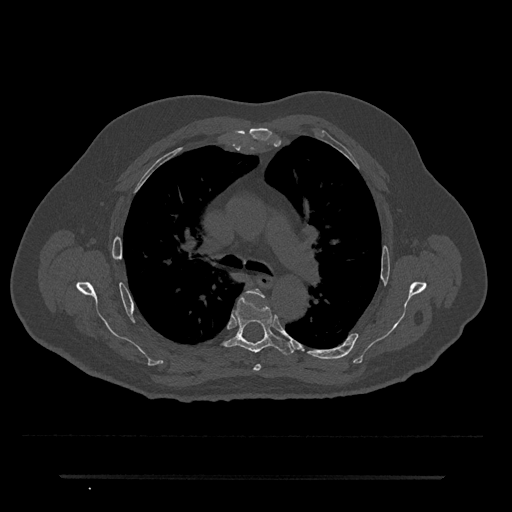
CT including the spine, one axial slice. Position 489 of 797 along the scan axis. Reconstruction kernel Br40s/3. Bone window (W 1800 / L 400 HU). 512 × 512 image matrix. Male patient, age 69 years. Case-level facts recorded for this patient, not image findings: primary cancer: prostate.
Structures marked on this image (semi-automatic segmentation, software-assisted and operator-edited):
- T4 vertebra: box from (x=244, y=289) to (x=264, y=371) px
- T5 vertebra: (x=224, y=293)–(x=294, y=355)